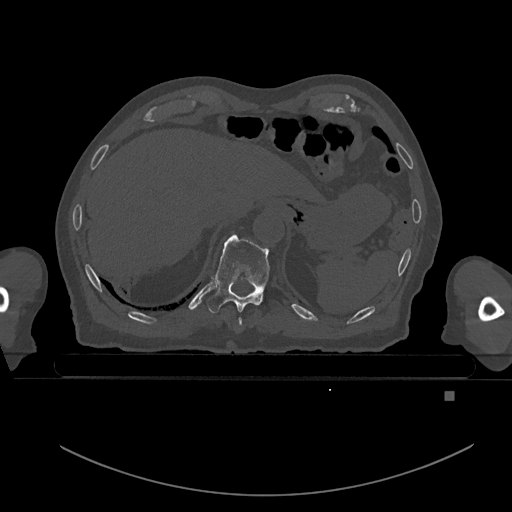
CT including the spine, one axial slice; slice 90 of 969 in the series (ordered by position); bone window (W 1800 / L 400 HU); 512 × 512 image matrix, field of view 456 × 456 mm. Male patient, age 82 years. Case-level facts recorded for this patient, not image findings: primary cancer: prostate; vertebrae with lytic lesions (as recorded): T11, T9, T8, T2.
Structures marked on this image (semi-automatic segmentation, software-assisted and operator-edited):
- T10 vertebra: box from (x=207, y=234) to (x=269, y=313) px
- T9 vertebra: (x=238, y=317)–(x=242, y=327)